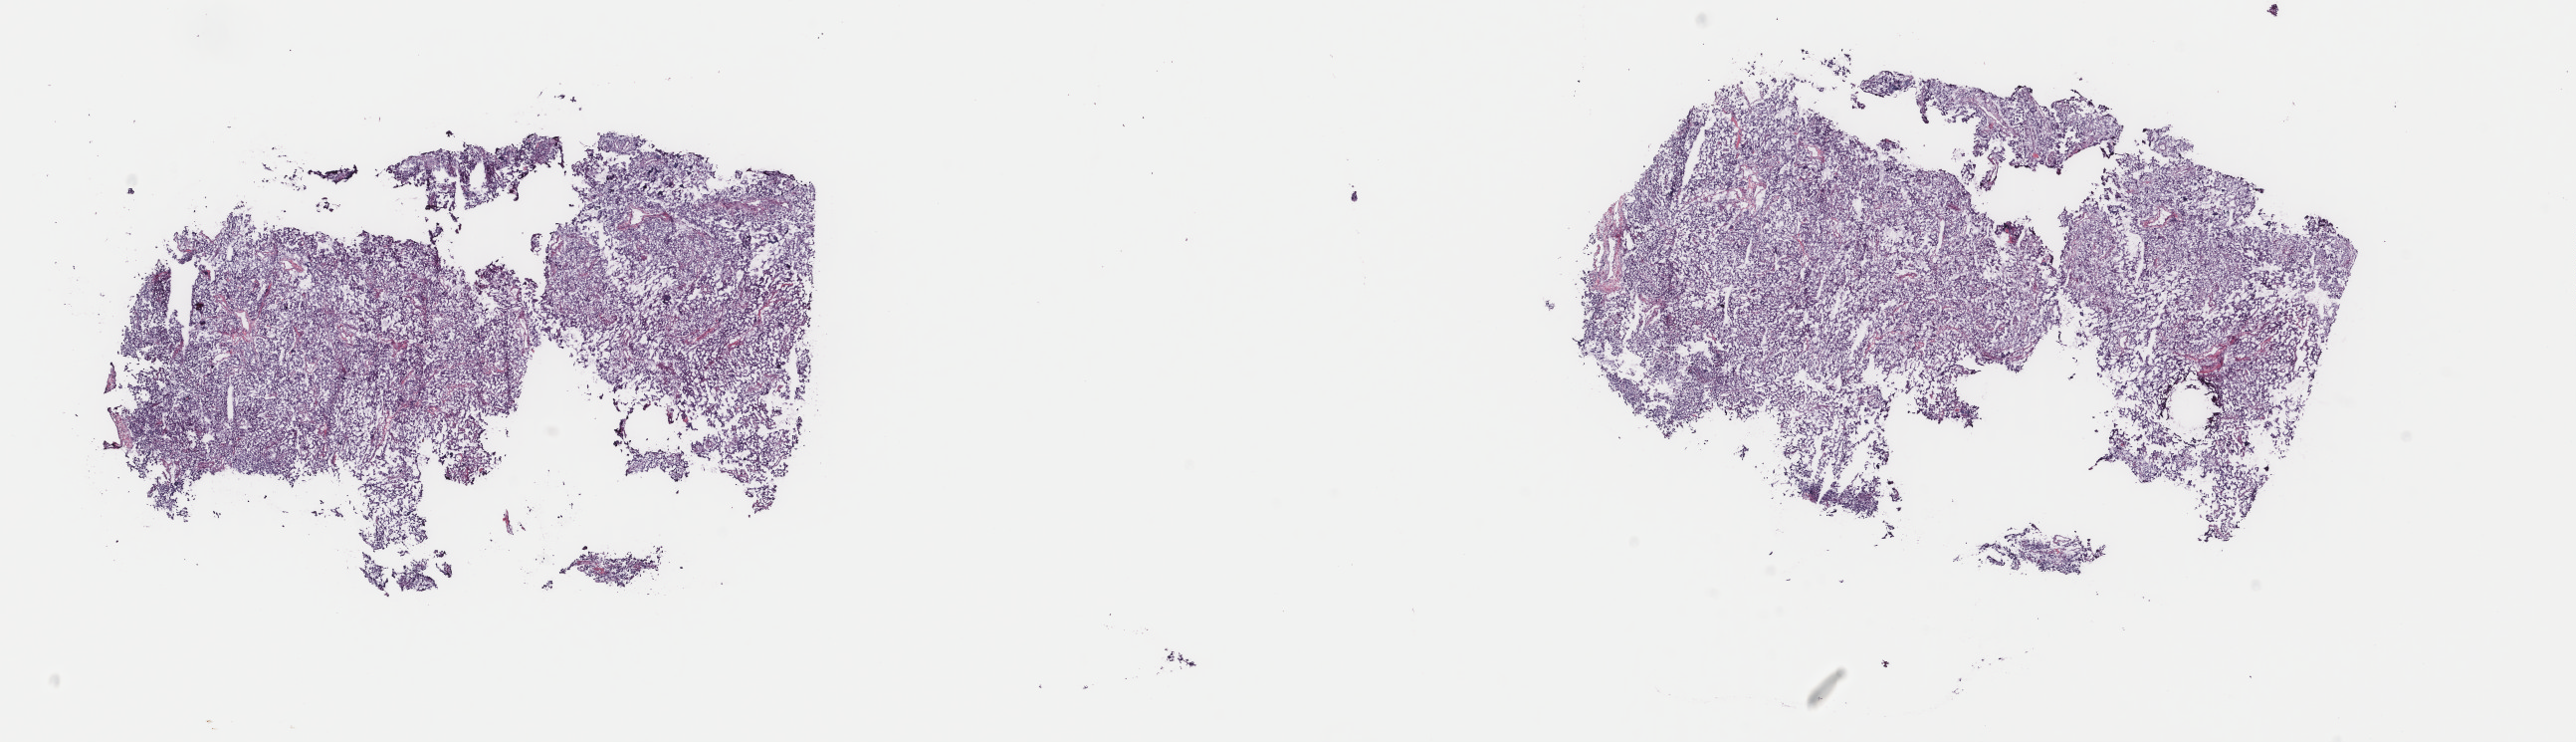
Whole-slide histology image, Hematoxylin and eosin (H&E) stained, low-resolution overview of the scanned area, about 20.5 x 5.9 mm; frozen section from the top of the tissue portion; adrenal gland, primary tumour sample. Male, age 33 years at initial diagnosis. Slide review estimates, as recorded: tumour cells 100%, tumour nuclei 95%, normal cells 0%, stromal cells 0%, necrosis 0%. Infiltration values recorded for this section: lymphocyte infiltration 0%, monocyte infiltration 0%, neutrophil infiltration 0%.
• pathologic diagnosis: Pheochromocytoma, NOS